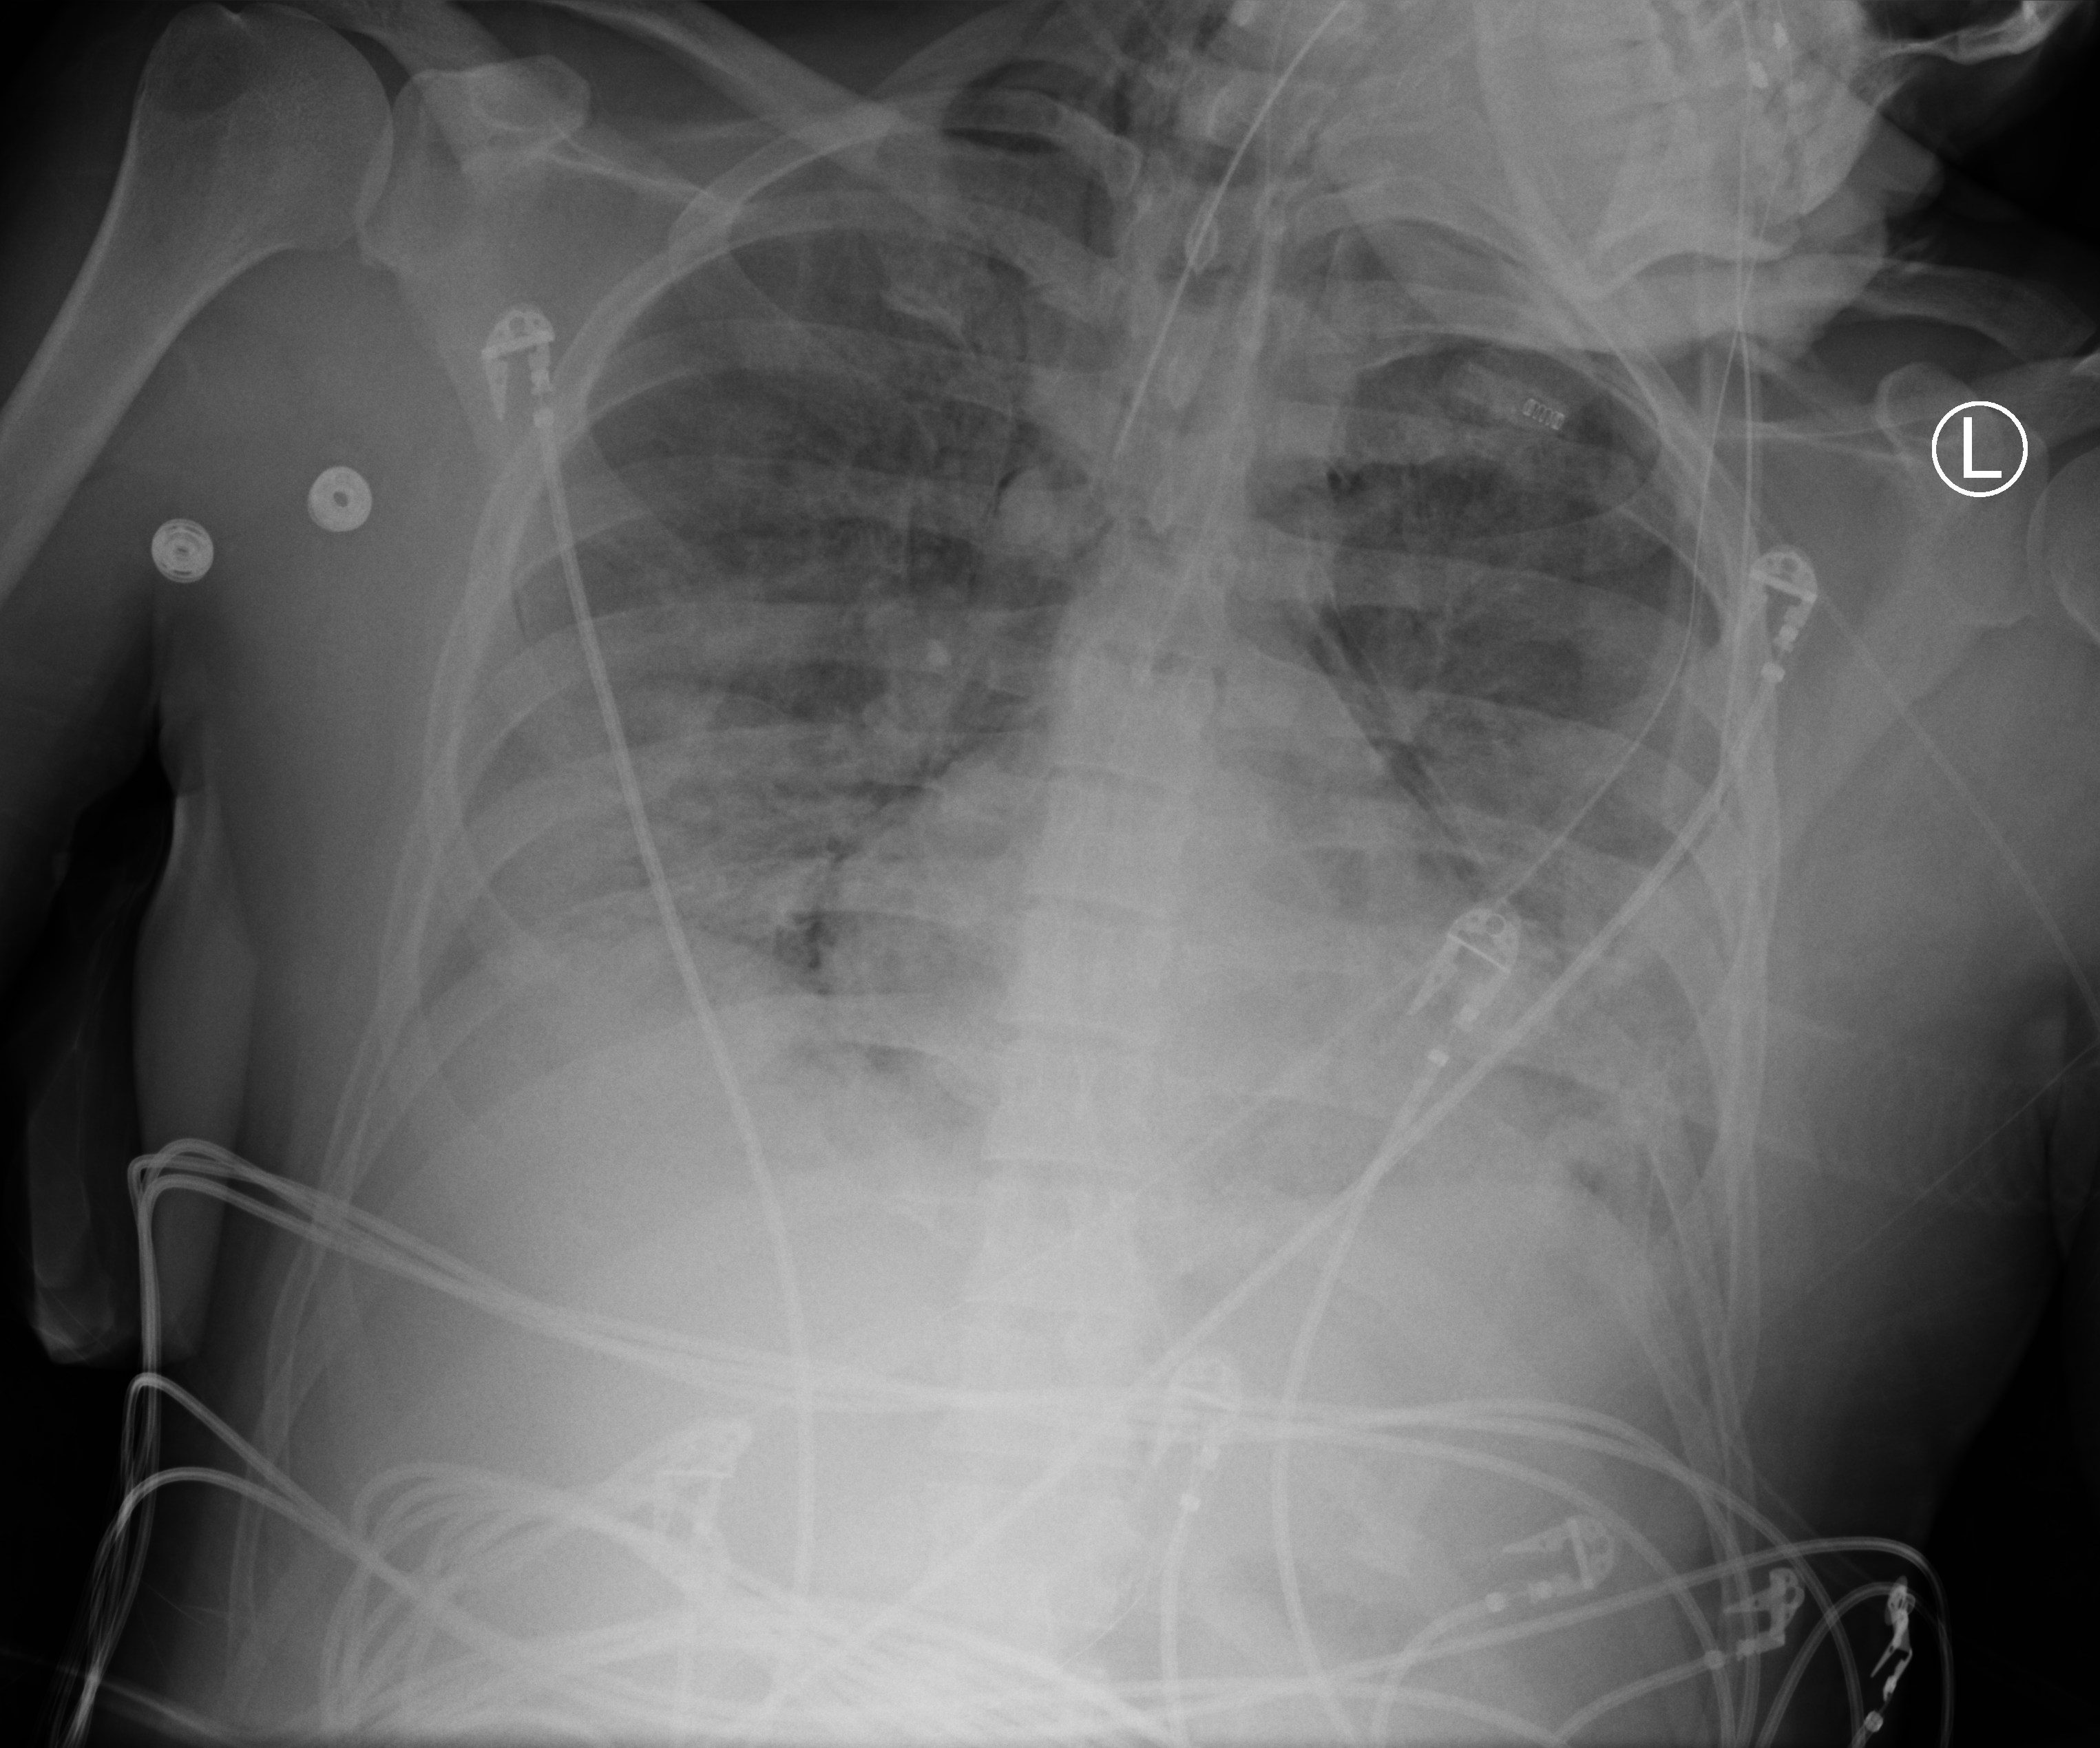
Chest X-ray (portable); anteroposterior (AP) projection. Patient hospitalised with COVID-19; male, aged 18–59 years.
Hospital-stay facts (about this admission, not read from this image; timing relative to this image not recorded): mechanically ventilated during this hospital stay: yes; smoking status (admission record): never; COPD (admission record): no.